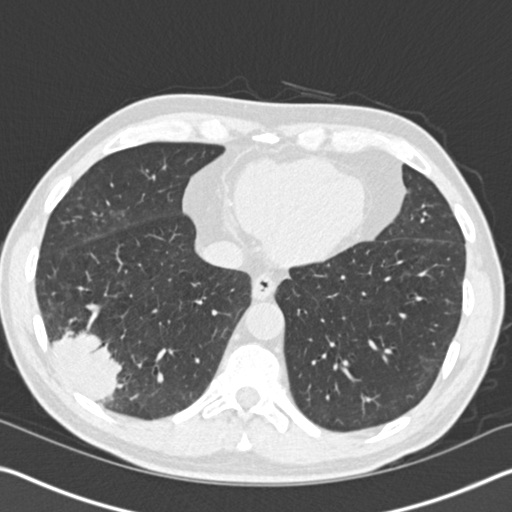
Axial slice from a low-dose chest CT screening exam; baseline annual screen; lung window (W 1500 / L -600 HU); 2 mm slice thickness; 120 kVp. Male, age 61 years at enrolment. Current smoker at enrolment.
Lesion marked by an expert reader, bounding box [x1, y1, x2, y2] px = [23, 293, 144, 418]. The exam's reader record, not a measurement of the box and not confirmed to be the same lesion: non-calcified nodule or mass ≥4 mm, right lower lobe, 52 × 36 mm, spiculated (stellate) margins, soft tissue attenuation. Later outcome: lung cancer diagnosed 392 days after this screen (after the second annual screen) — bronchiolo-alveolar adenocarcinoma, NOS, right lower lobe, moderately differentiated (G2), stage IIIB (AJCC 6th edition), 90 mm at pathology.